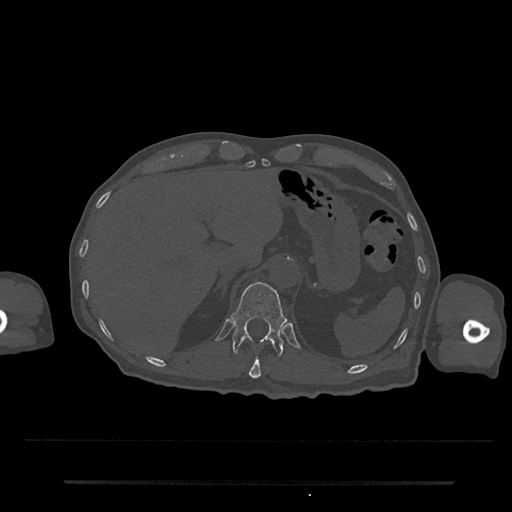
CT including the spine, one axial slice. Position 213 of 797 along the scan axis. Bone window (W 1800 / L 400 HU). 0.5 mm slice thickness. 512 × 512 image matrix. Male patient, age 74 years. Case-level facts recorded for this patient, not image findings: primary cancer: prostate.
Annotated regions visible in this slice (semi-automatically segmented with operator editing):
- T11 vertebra: bounding box (x1, y1, x2, y2) in pixels: (249, 356, 261, 379)
- T12 vertebra: (231, 282, 287, 356)